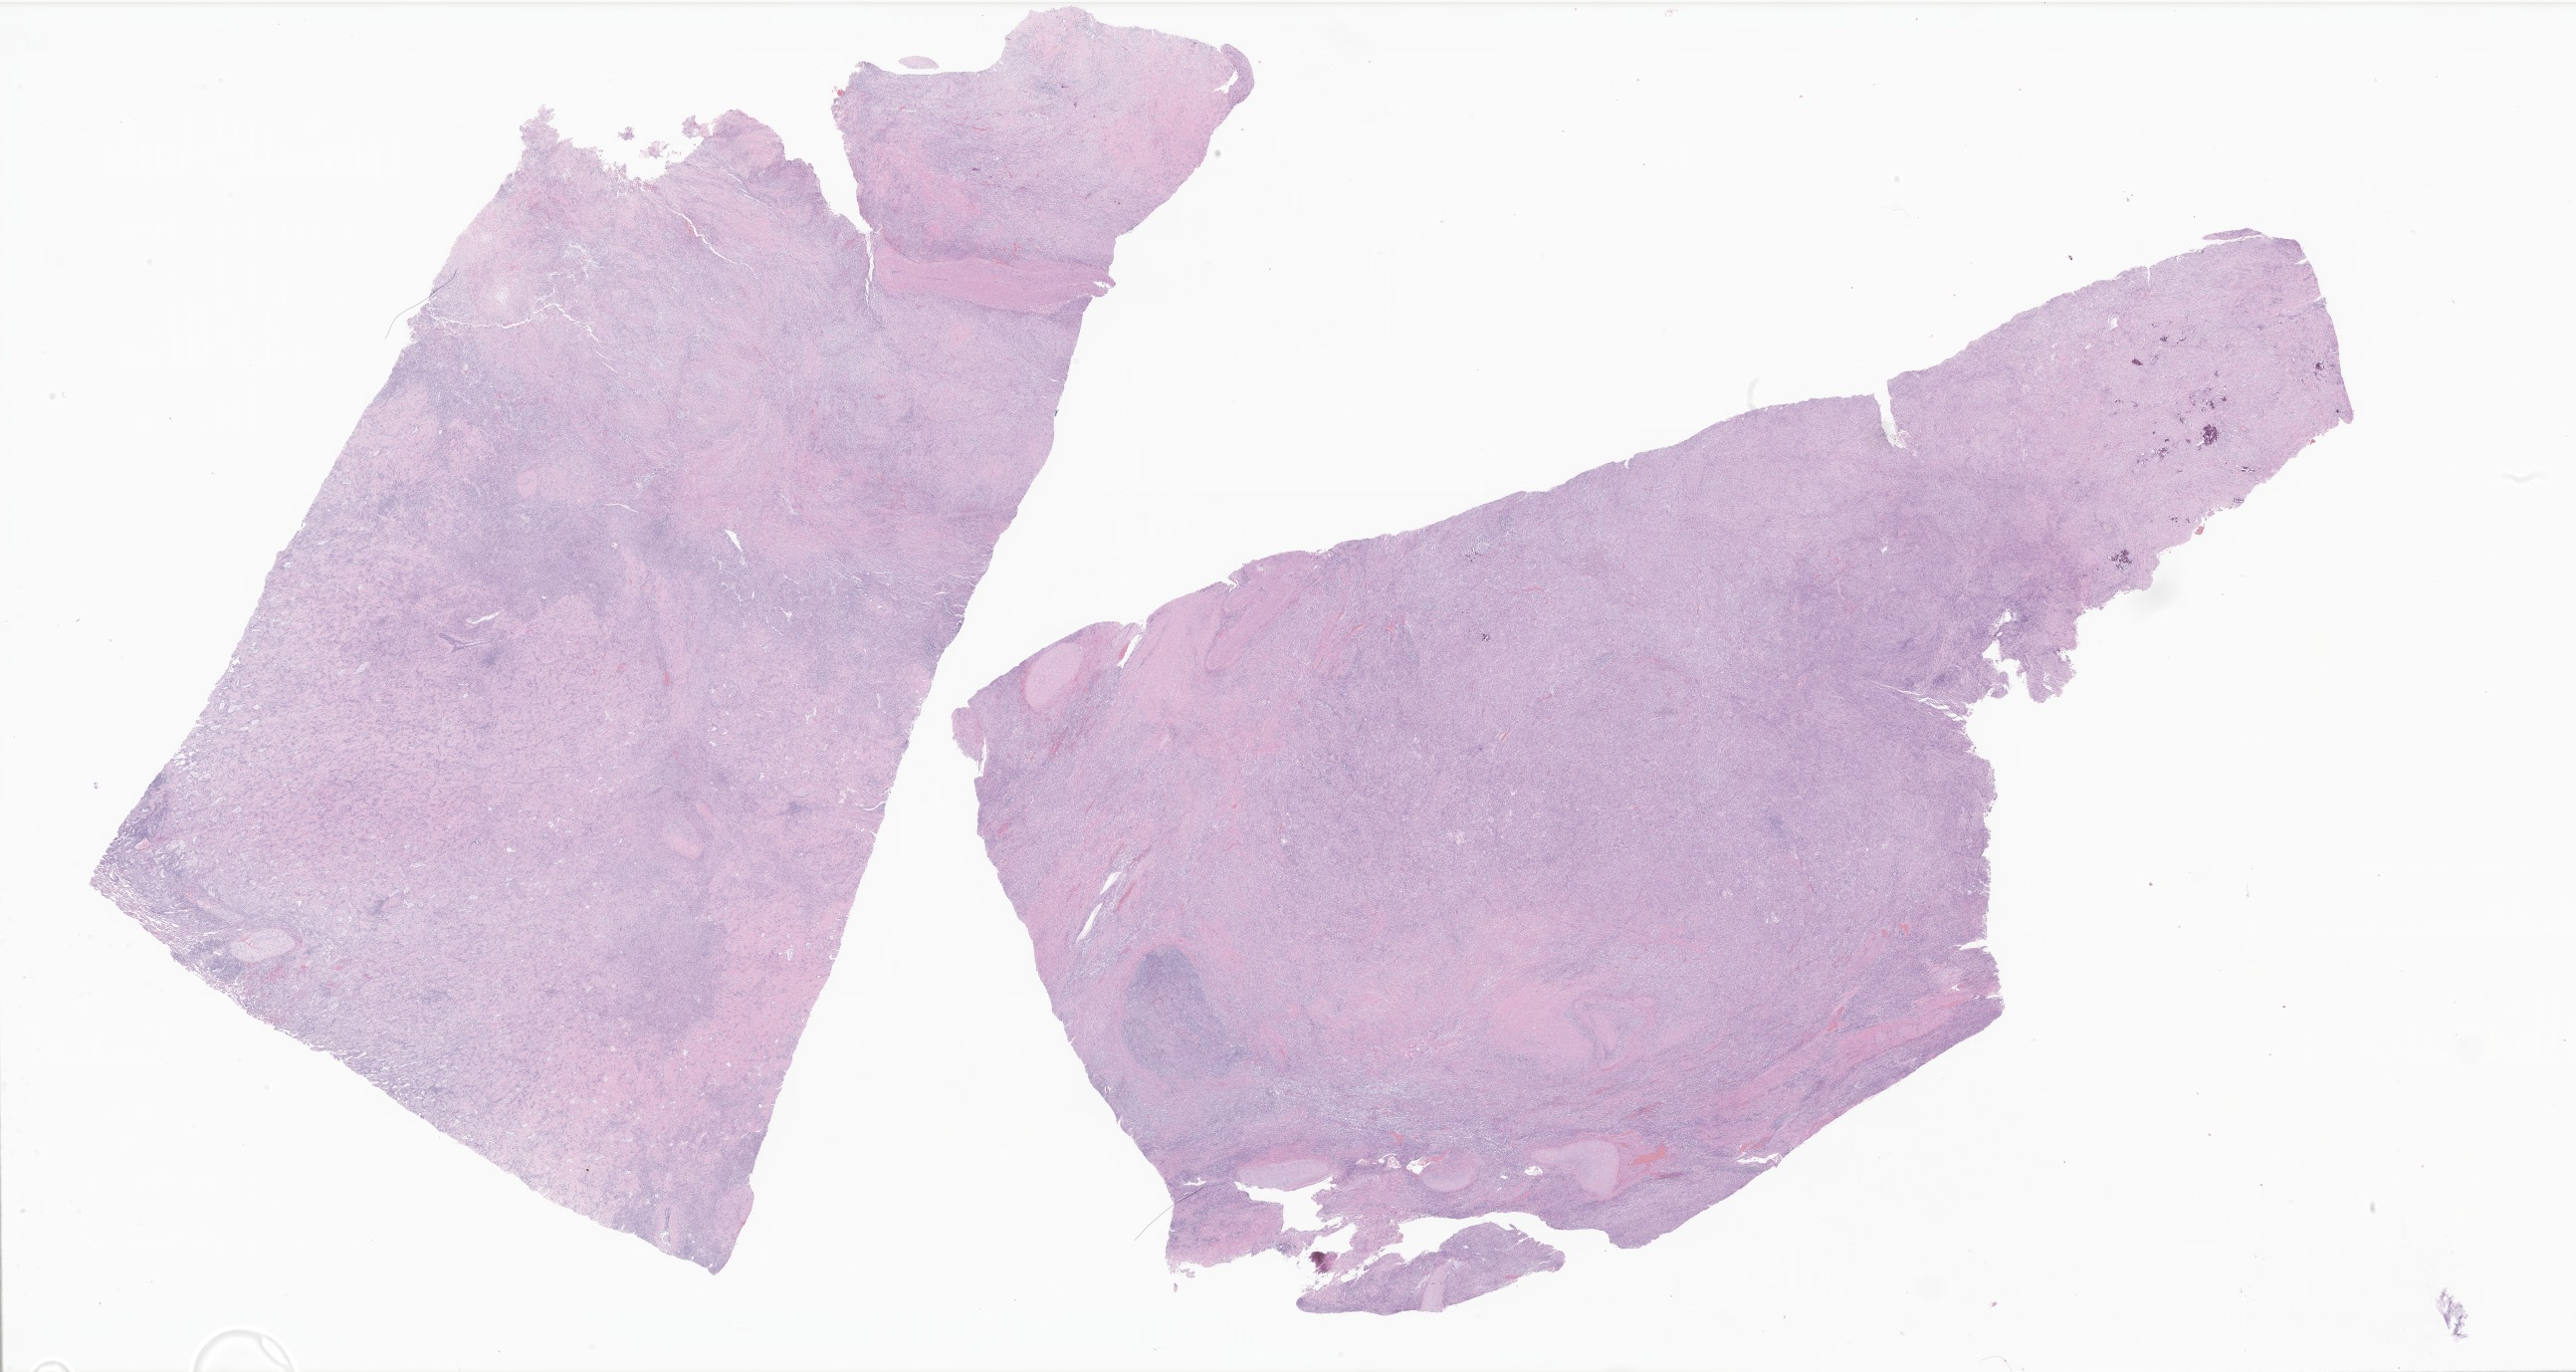
Digitized haematoxylin and eosin-stained section of tumor tissue from the lower lobe of lung, whole scanned area (about 43.6 x 23.2 mm) shown as a low-resolution overview, formalin-fixed paraffin-embedded section. Patient: female, age 247 months (20 years 7 months).
Recorded diagnosis: Myofibroblastic tumor, NOS.